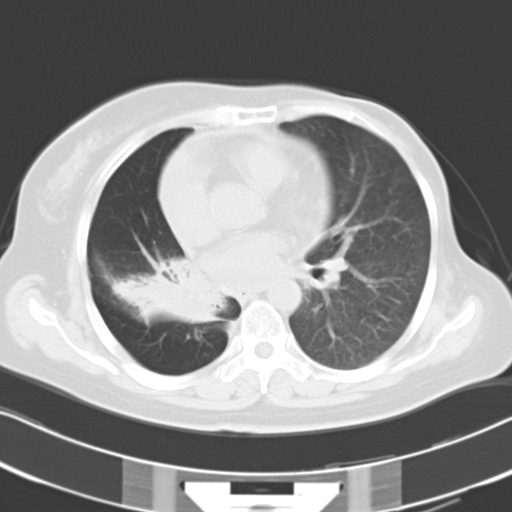
Chest CT, one axial slice. Slice 16 of 30 in the series (ordered by position). Reconstruction kernel B40f. 120 kVp. Lung window (W 1500 / L -600 HU). 8 mm slice thickness. 512 × 512 image matrix, field of view 331 × 331 mm. Female patient, age 53 years. From the clinical record (not read from this slice): clinical TNM (as recorded): T2b N1 M0.
Outlined on this slice (rectangle marked by the reading radiologist):
- lung tumour (recorded histology: adenocarcinoma): box from (x=108, y=253) to (x=226, y=330) px